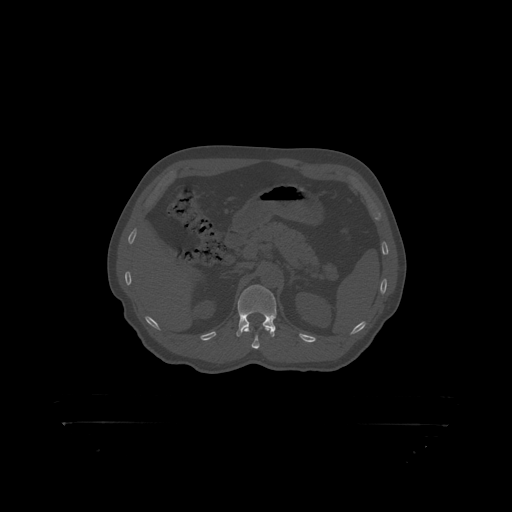
CT including the spine, one axial slice. Position 335 of 399 along the scan axis. Bone window (W 1800 / L 400 HU). 1.25 mm slice thickness. 512 × 512 image matrix, field of view 650 × 650 mm. Patient: male, 46 years. Case-level facts recorded for this patient, not image findings: primary cancer: skin.
Structures marked on this image (semi-automatically segmented with operator editing):
- L1 vertebra: bounding box (x1, y1, x2, y2) in pixels: (238, 285, 277, 319)